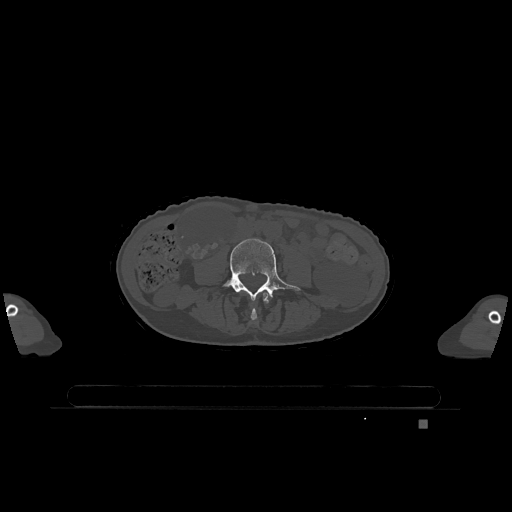
CT including the spine, one axial slice. Position 304 of 1317 along the scan axis. Bone window (W 1800 / L 400 HU). 512 × 512 image matrix, field of view 500 × 500 mm. Female patient, age 74 years. From the clinical record (not read from this slice): primary cancer: lung; vertebrae with lytic lesions (as recorded): T1, T4, T5, T6, L4, L5.
Outlined on this slice (semi-automatic segmentation, software-assisted and operator-edited):
- L3 vertebra: box from (x=246, y=291) to (x=270, y=321) px
- L4 vertebra: (x=222, y=238)–(x=300, y=301)